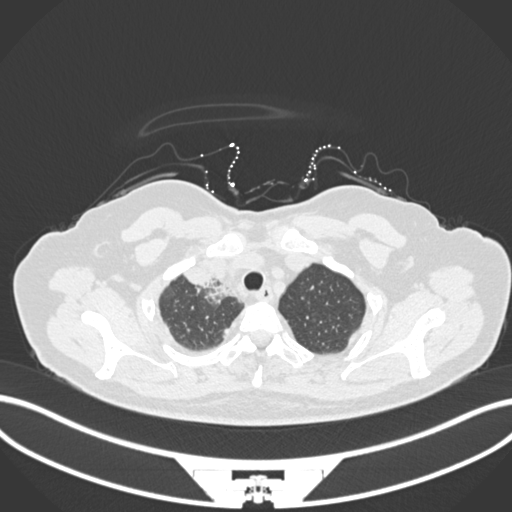
Chest CT, one axial slice; position 146 of 172 along the scan axis; 120 kVp; lung window (W 1500 / L -600 HU); 1 mm slice thickness; 512 × 512 image matrix, field of view 400 × 400 mm. Patient: female, 52 years. From the clinical record (not read from this slice): clinical TNM (as recorded): T3 N1 M1.
Annotated regions visible in this slice (rectangle marked by the reading radiologist):
- lung tumour (recorded histology: adenocarcinoma): bounding box <183,265,229,300> (left, top, right, bottom; pixels)